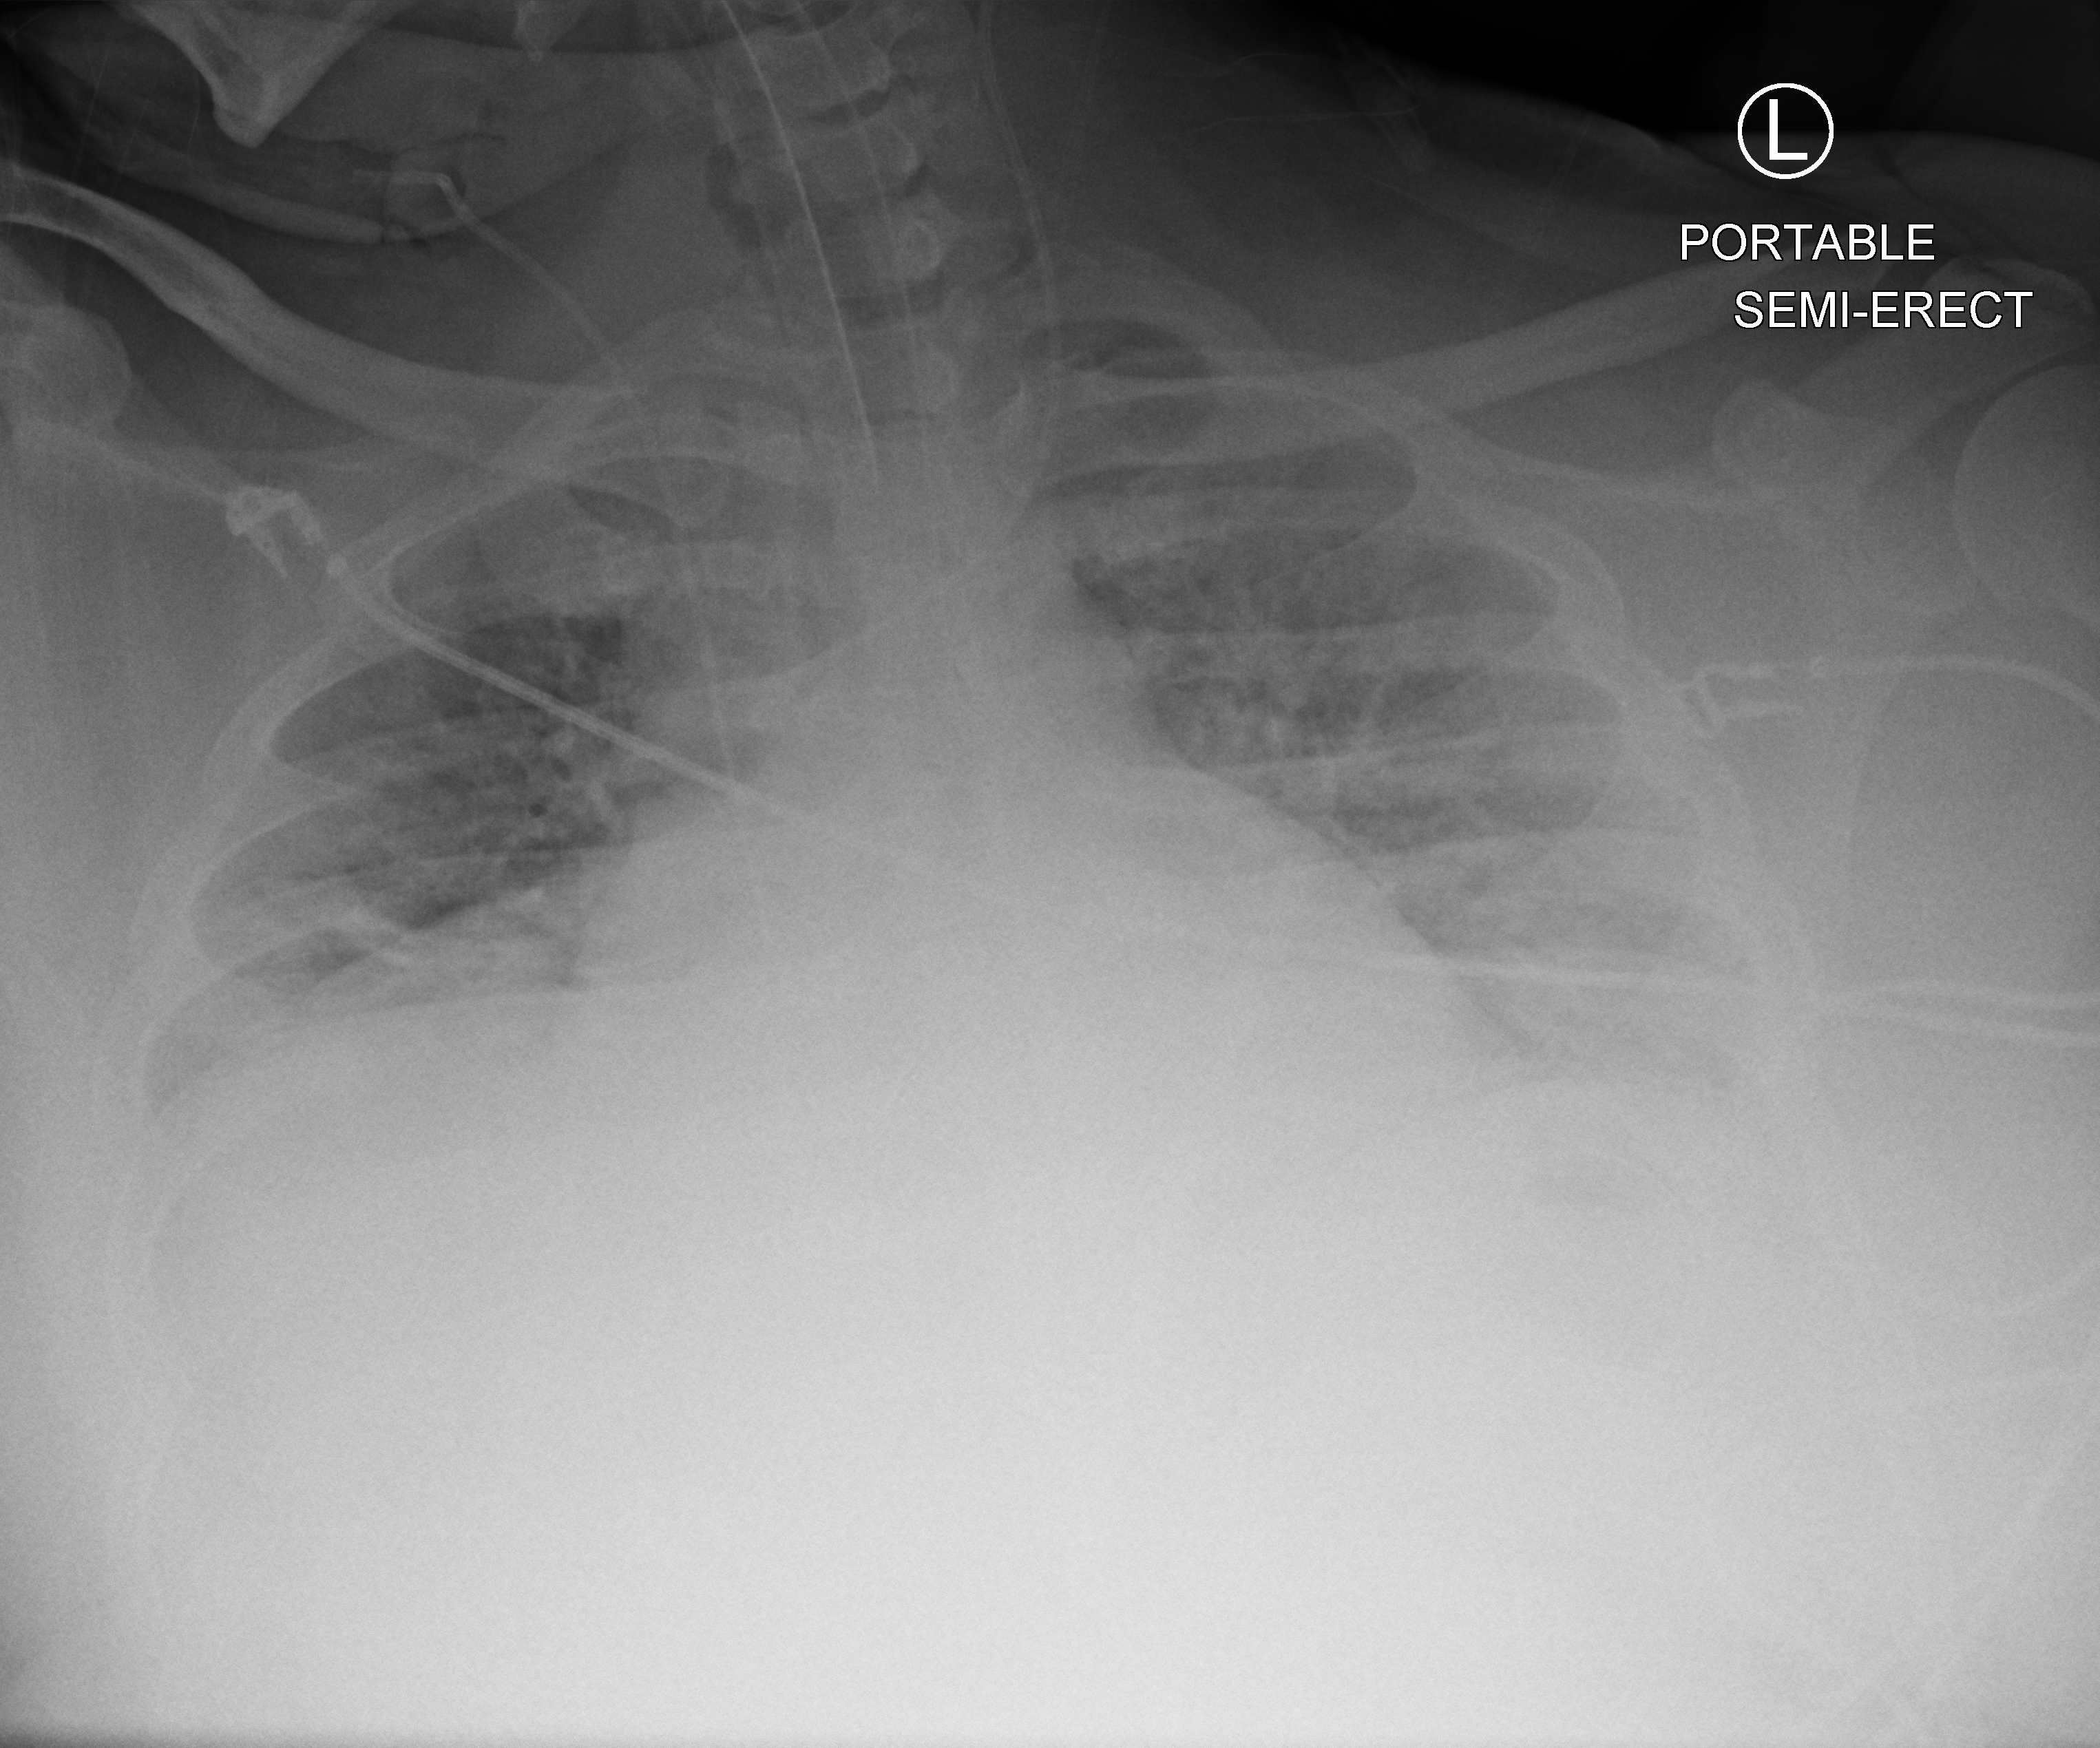
Chest X-ray (portable); anteroposterior (AP) projection. Patient hospitalised with COVID-19; male, aged 18–59 years.
Admission-level facts for this patient (not findings on this image; timing relative to this image not recorded): length of hospital stay: 69 days; chronic kidney disease (admission record): no; admitted to intensive care during this hospital stay: yes.